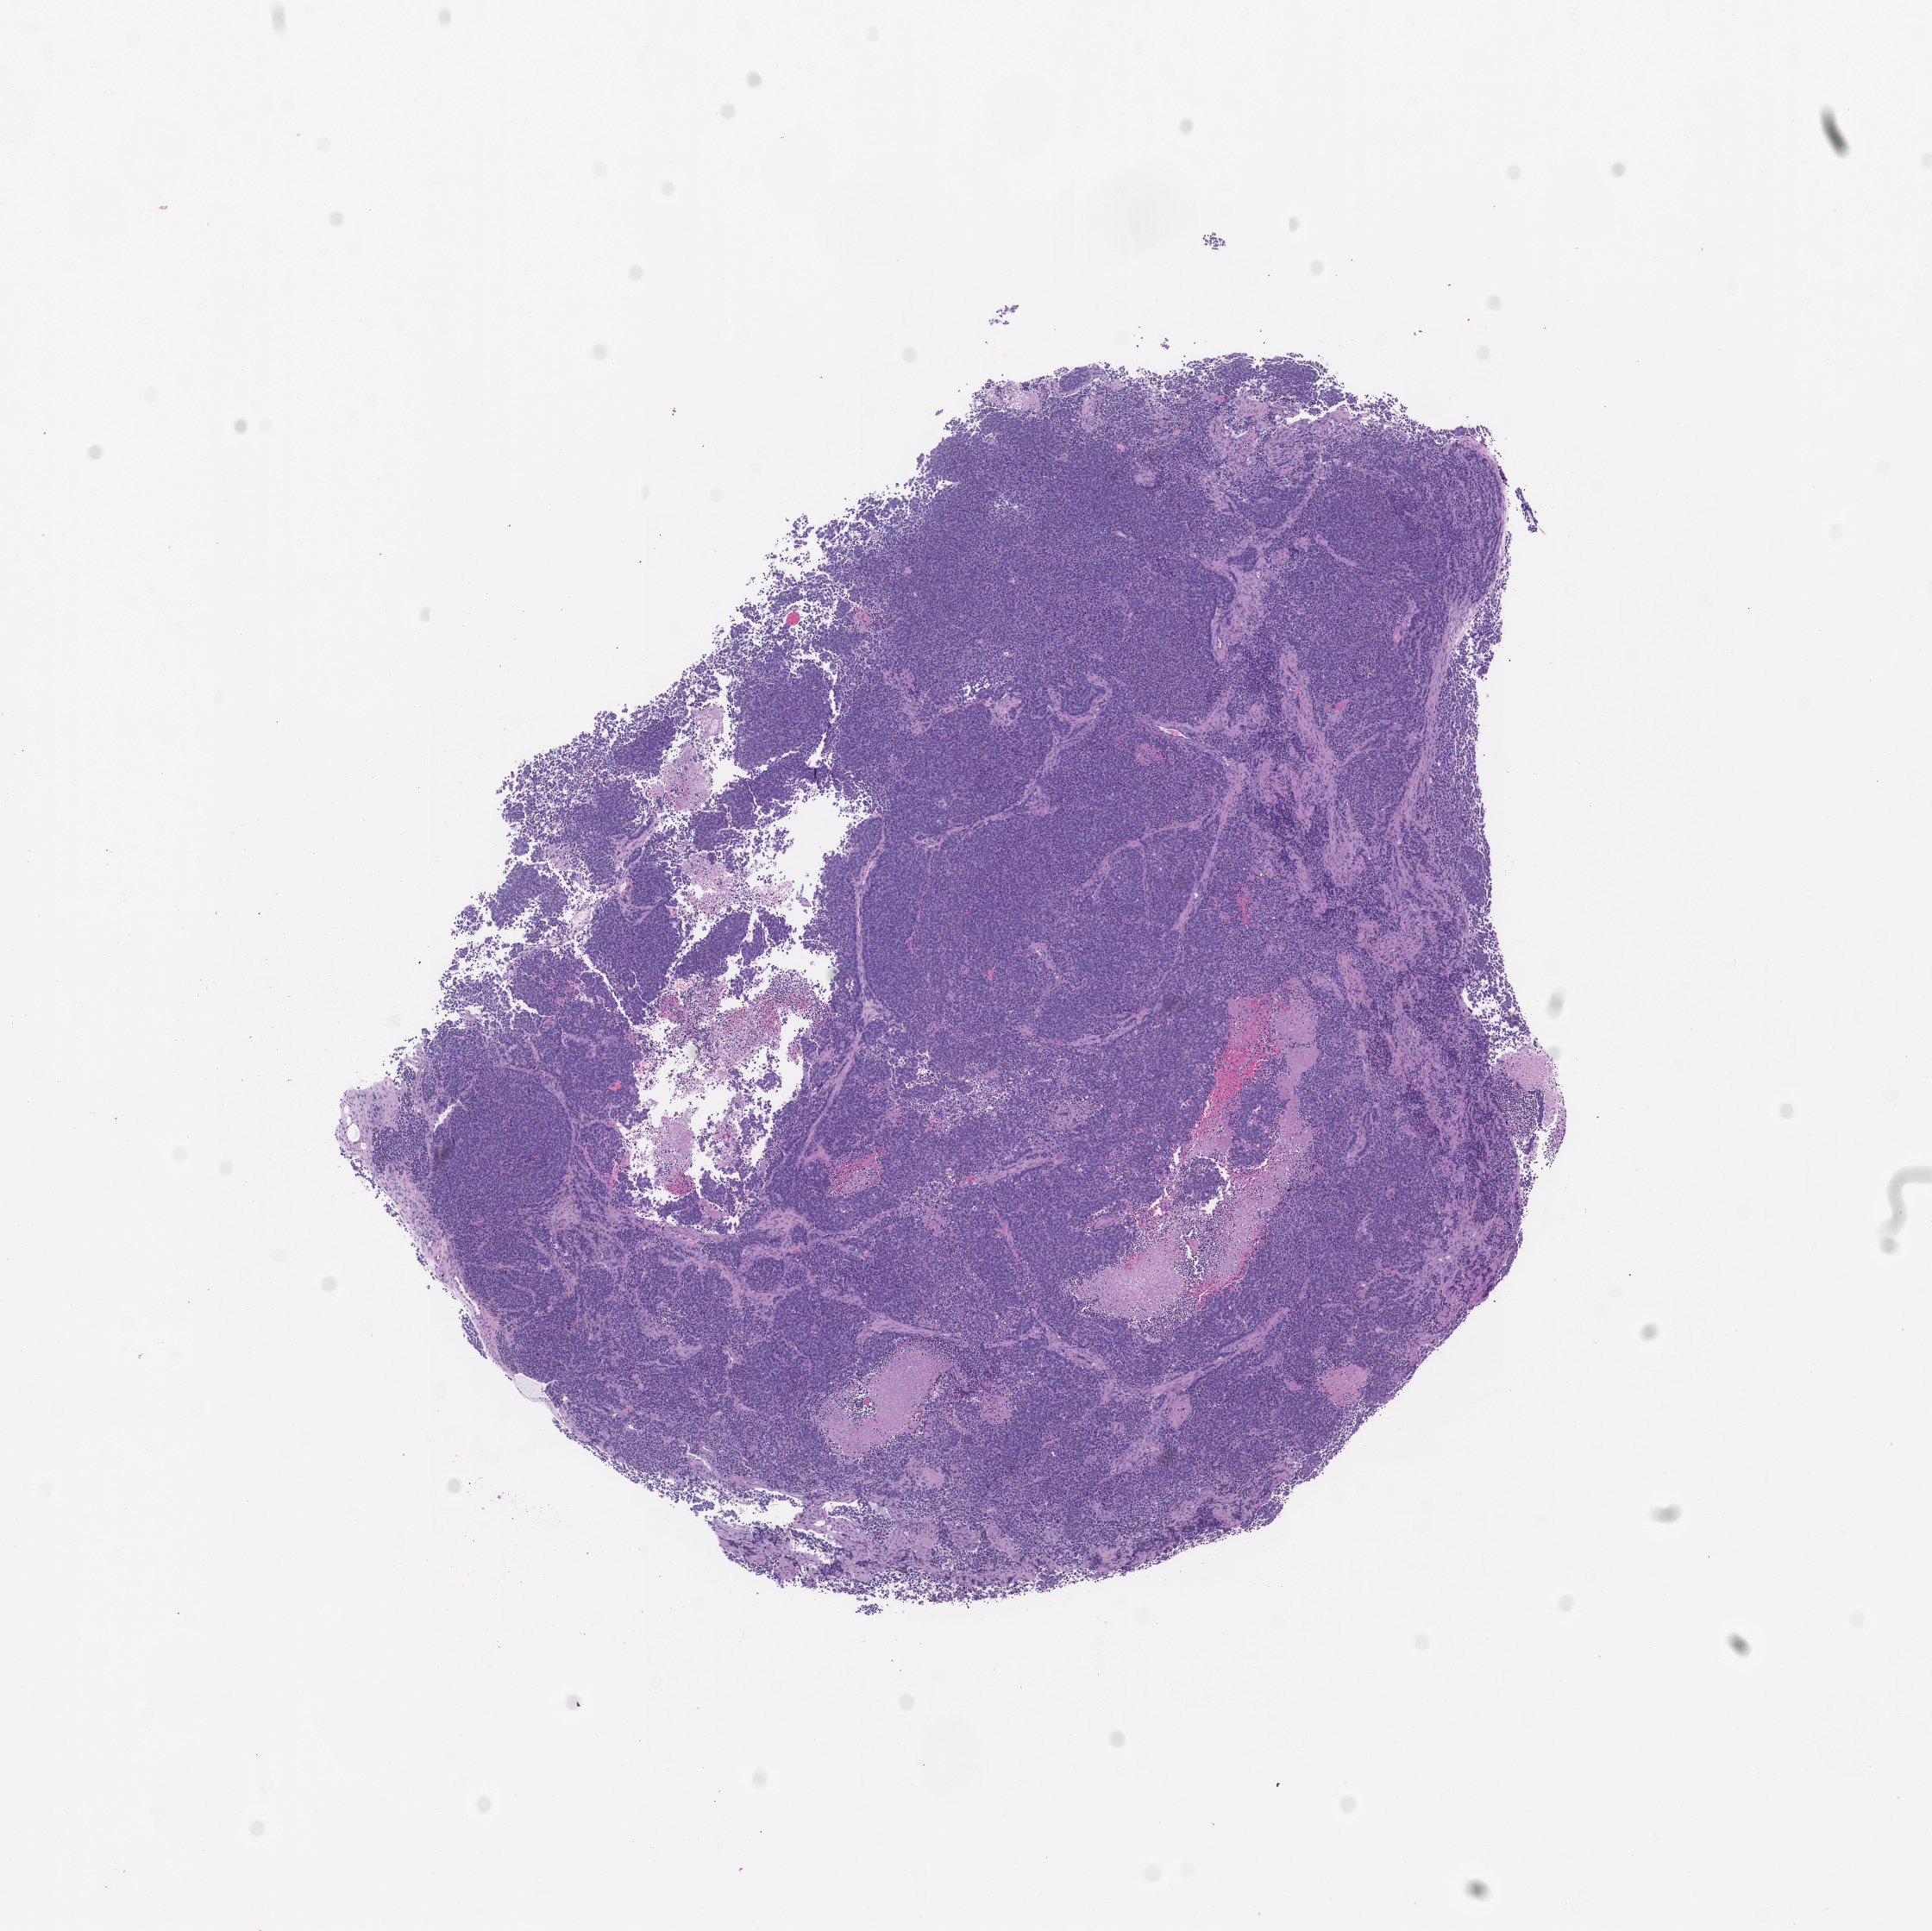
Hematoxylin and eosin (H&E) whole-slide image of a patient-derived xenograft (PDX) tumor grown in a mouse, passage 1, low-resolution overview of the scanned area, about 9.0 x 9.0 mm, formalin-fixed paraffin-embedded section, originating tumor site category: bladder.
• originating patient diagnosis: Bladder Small Cell Neuroendocrine Carcinoma